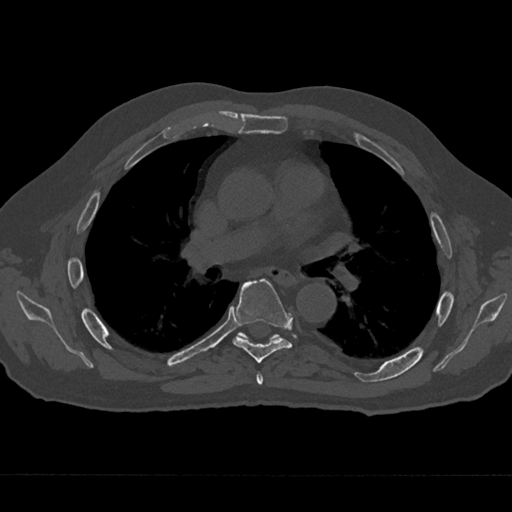
CT including the spine, one axial slice; reconstruction kernel Br40s/3; bone window (W 1800 / L 400 HU); 512 × 512 image matrix, field of view 377 × 377 mm. Male patient, age 75 years. Case-level facts recorded for this patient, not image findings: primary cancer: renal.
Structures marked on this image (semi-automatic segmentation, software-assisted and operator-edited):
- T5 vertebra: bounding box (x1, y1, x2, y2) in pixels: (256, 372, 263, 385)
- T6 vertebra: (232, 279, 293, 363)
- T7 vertebra: (239, 333, 278, 340)